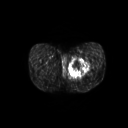
FDG PET of an extremity soft-tissue mass (from a PET/CT study), one axial slice; position 31 of 267 along the scan axis; 3.27 mm slice thickness; 128 × 128 image matrix. Patient: male, 59 years. Case-level facts recorded for this patient, not image findings: histological type: pleiomorphic liposarcoma; grade: high; site of the primary tumour: left thigh.
Annotated regions visible in this slice (expert contour drawn on MRI and transferred to this co-registered scan by the dataset authors):
- gross tumour volume including surrounding oedema: bounding box <69,57,90,78> (left, top, right, bottom; pixels)
- gross tumour volume (mass): <69,58,90,77>